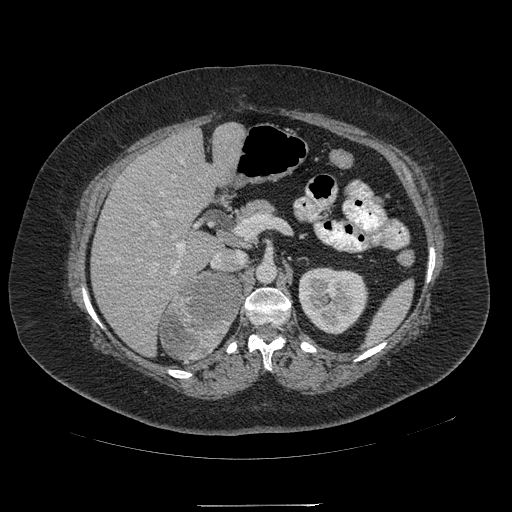
Contrast-enhanced abdominal CT, one axial slice; position 124 of 217 along the scan axis; reconstruction kernel STANDARD; intravenous contrast given; soft-tissue window (W 400 / L 40 HU); 1.25 mm slice thickness; 512 × 512 image matrix. Patient: female, 55 years. Case-level facts recorded for this patient, not image findings: diagnosis: adrenocortical carcinoma; tumour side: right adrenal; tumour size at pathology: 11 cm; Ki-67 index: 20 %; stage (as recorded): 2.
Outlined on this slice (semi-automatic segmentation, software-assisted and operator-edited):
- mass: bounding box [x1, y1, x2, y2] px = [160, 272, 241, 359]